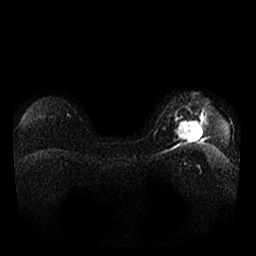
Breast MRI, one axial slice. Slice 19 of 25 in the series (ordered by position). Diffusion-weighted series; image 2 of 4 stored at this slice position (different b-values; order by instance number). 1.5 T. 4 mm slice thickness. 256 × 256 image matrix, field of view 340 × 340 mm. Female patient.
Outlined on this slice (outlined manually by an expert reader):
- tumour on diffusion-weighted imaging: bounding box <177,116,202,143> (left, top, right, bottom; pixels)